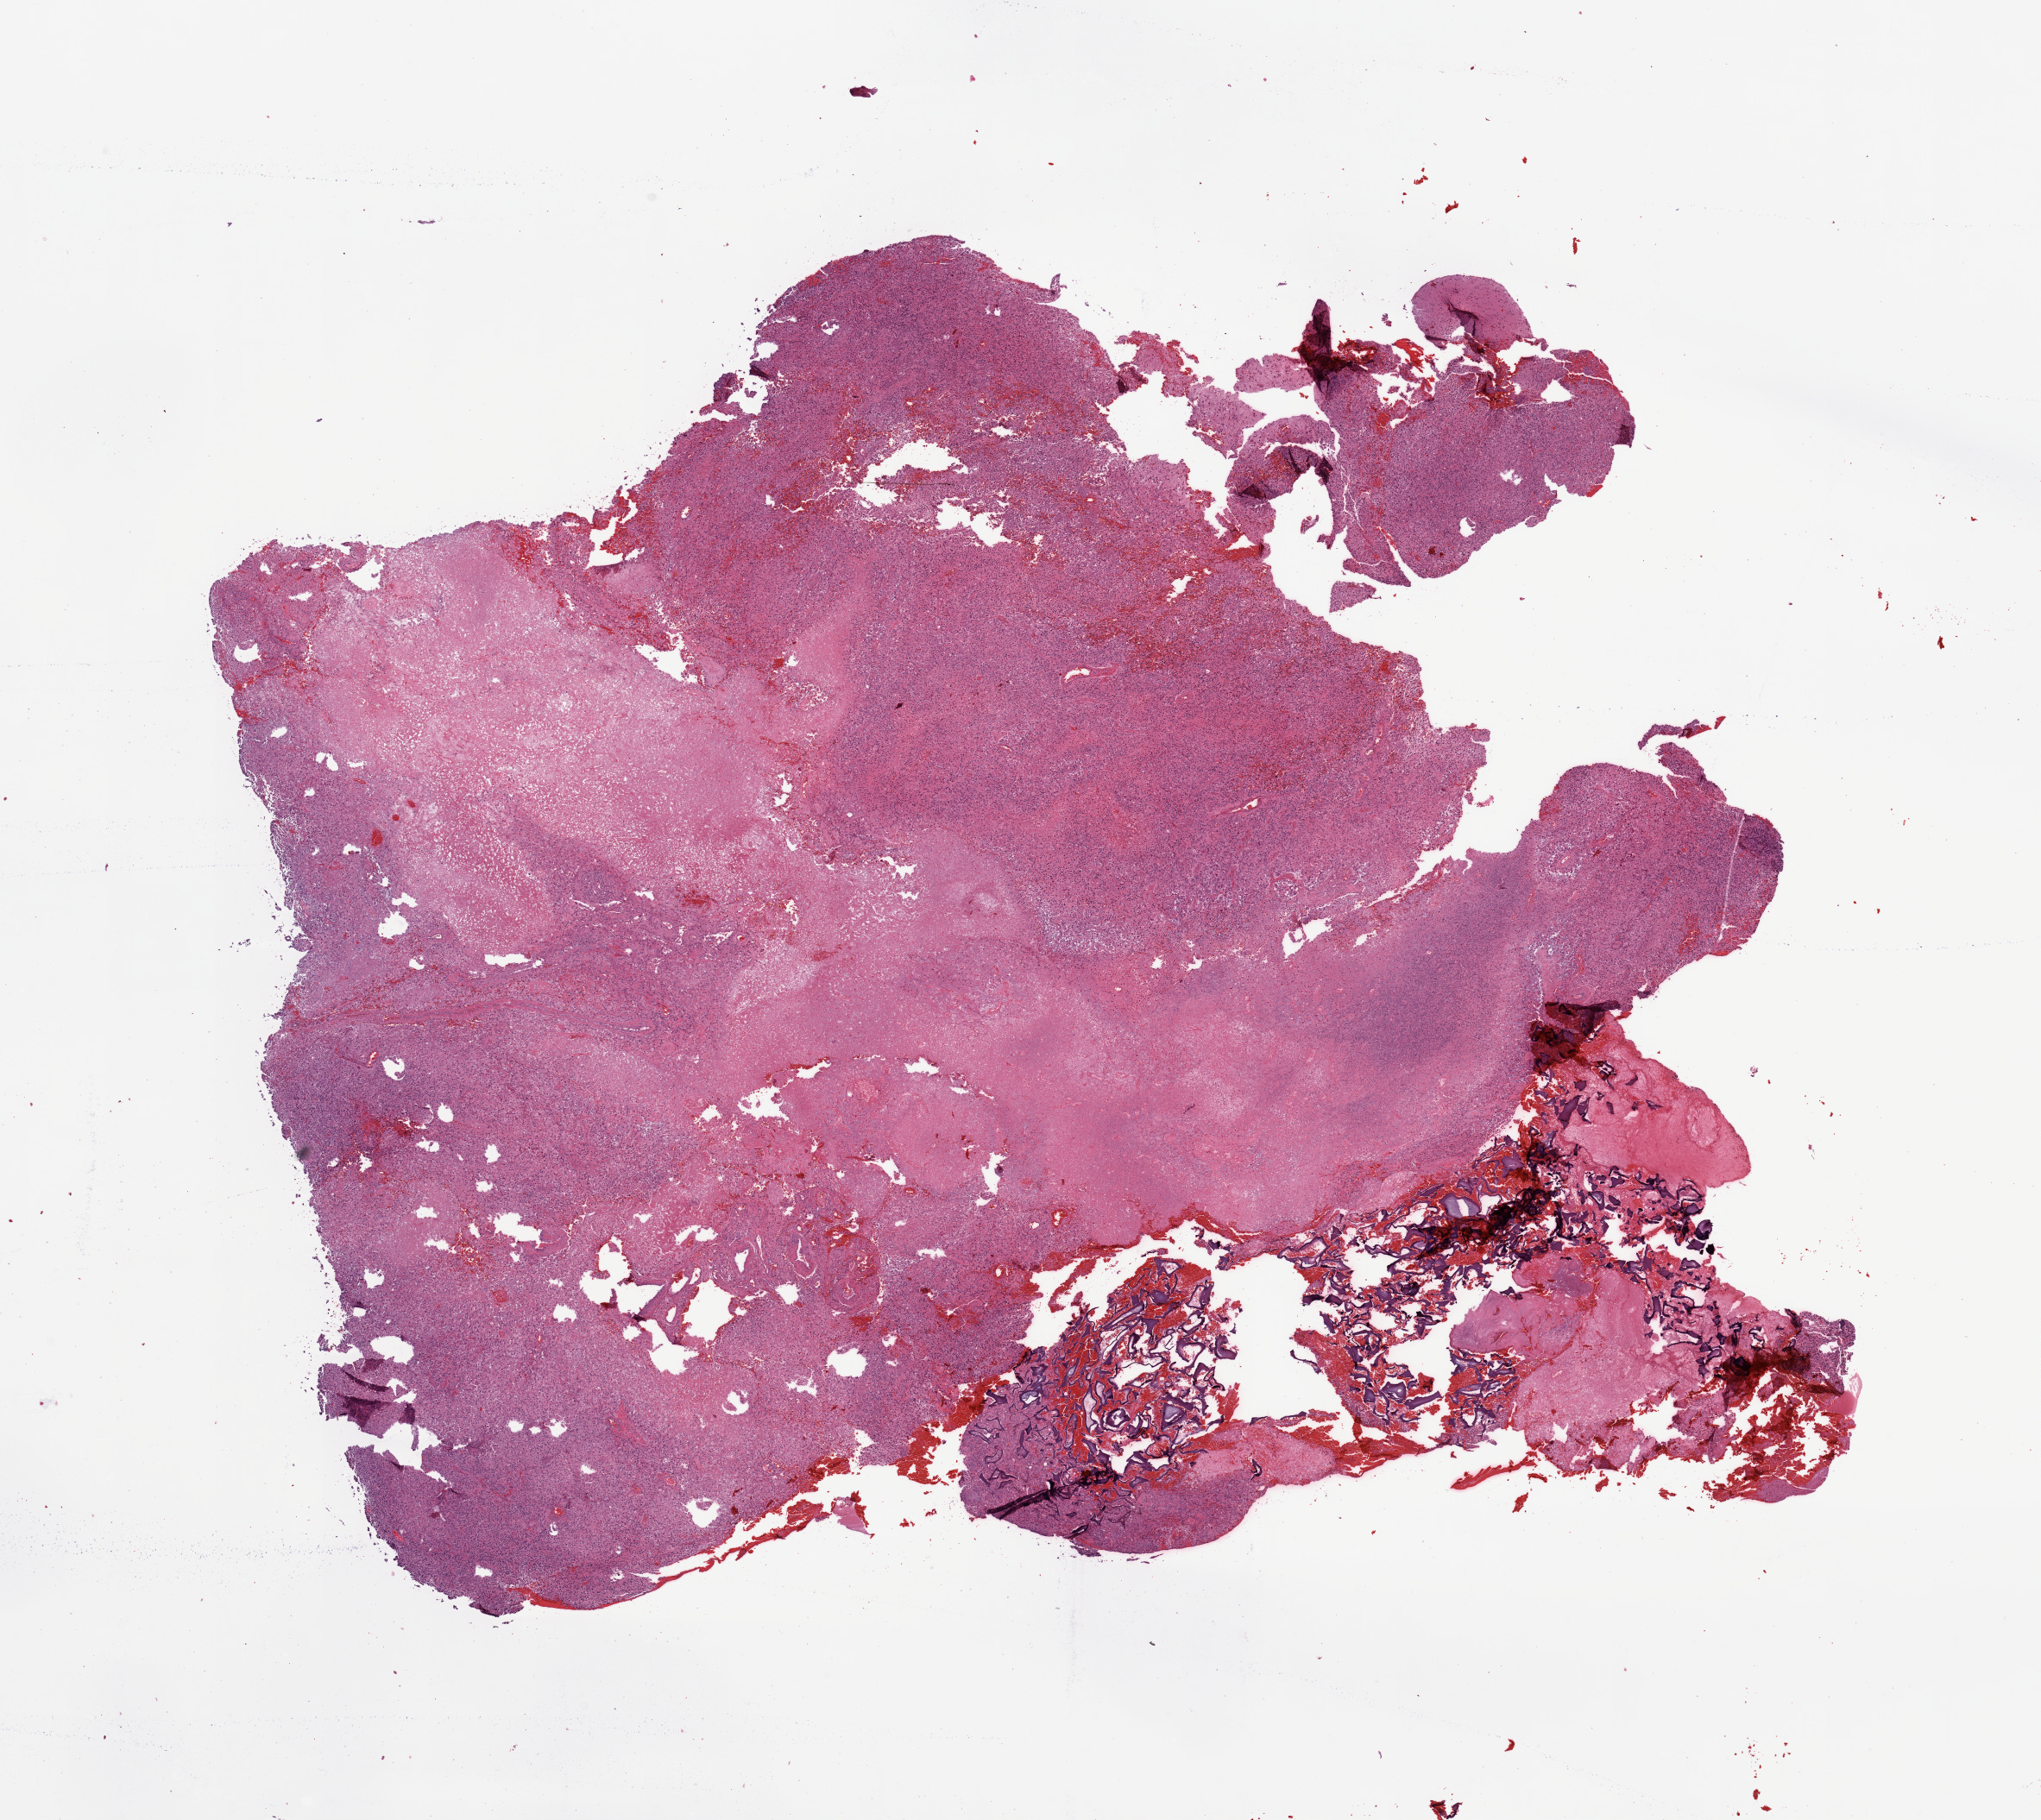
Digitized Hematoxylin and eosin (H&E) stained tissue section (whole slide) — low-resolution overview of the scanned area, about 18.7 x 16.7 mm, brain, tumour tissue. 60-year-old male patient.
Histologic diagnosis: Glioblastoma. Primary tumour site (as recorded): frontal lobe.